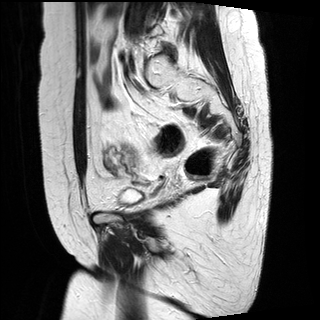
Pelvic MRI for cervical cancer, one sagittal slice. Slice 10 of 29 in the series (ordered by position). T2-weighted. 1.5 T. TE 89 ms, TR 2930 ms. 4 mm slice thickness. 320 × 320 image matrix, field of view 260 × 260 mm. Female patient, age 49 years.
Outlined on this slice (outlined manually by an expert reader):
- uterus and cervix: bounding box [x1, y1, x2, y2] px = [122, 144, 141, 161]